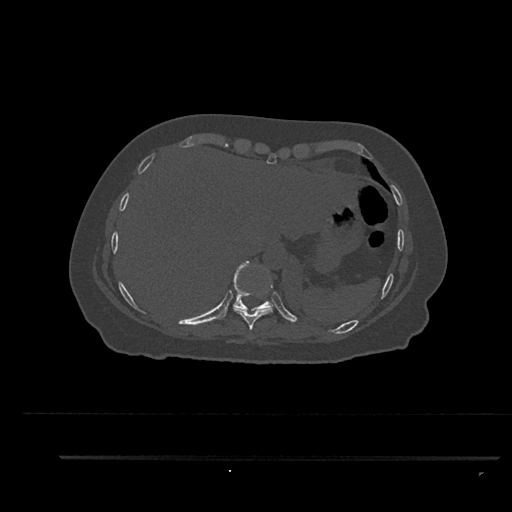
CT including the spine, one axial slice; position 394 of 797 along the scan axis; 120 kVp; bone window (W 1800 / L 400 HU); 0.5 mm slice thickness; 512 × 512 image matrix, field of view 408 × 408 mm. Female patient, age 44 years. From the clinical record (not read from this slice): primary cancer: renal; vertebrae with lytic lesions (as recorded): L1.
Outlined on this slice (semi-automatically segmented with operator editing):
- T10 vertebra: bounding box (x1, y1, x2, y2) in pixels: (233, 260, 274, 311)
- T9 vertebra: (233, 307, 273, 330)